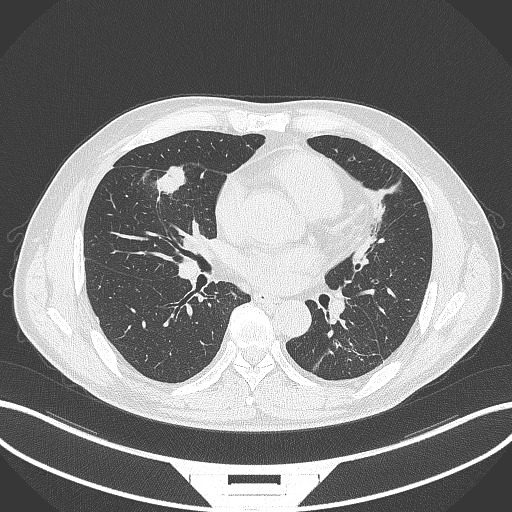
Chest CT, one axial slice; slice 147 of 399 in the series (ordered by position); reconstruction kernel B70f; 120 kVp; lung window (W 1500 / L -600 HU); 1 mm slice thickness; 512 × 512 image matrix, field of view 400 × 400 mm. Patient: male, 59 years. Case-level facts recorded for this patient, not image findings: clinical TNM (as recorded): T2a N1 M0.
Structures marked on this image (bounding box drawn by a radiologist):
- lung tumour (recorded histology: adenocarcinoma): bounding box [x1, y1, x2, y2] px = [153, 161, 192, 198]